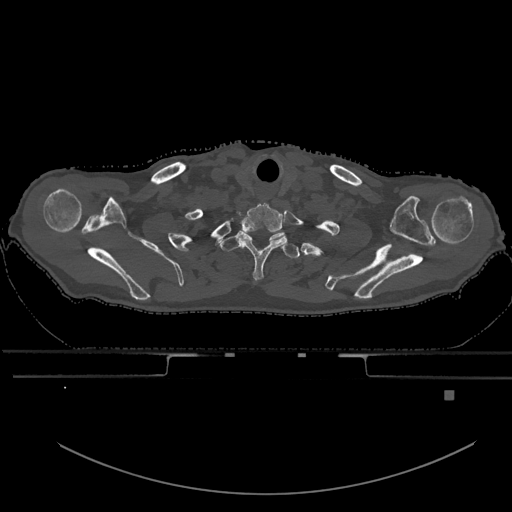
CT including the spine, one axial slice. Slice 558 of 969 in the series (ordered by position). Bone window (W 1800 / L 400 HU). 512 × 512 image matrix, field of view 456 × 456 mm. Patient: male, 82 years. Case-level facts recorded for this patient, not image findings: primary cancer: prostate; vertebrae with lytic lesions (as recorded): T11, T9, T8, T2.
Structures marked on this image (semi-automatic segmentation, software-assisted and operator-edited):
- T1 vertebra: bounding box <220,233,300,259> (left, top, right, bottom; pixels)